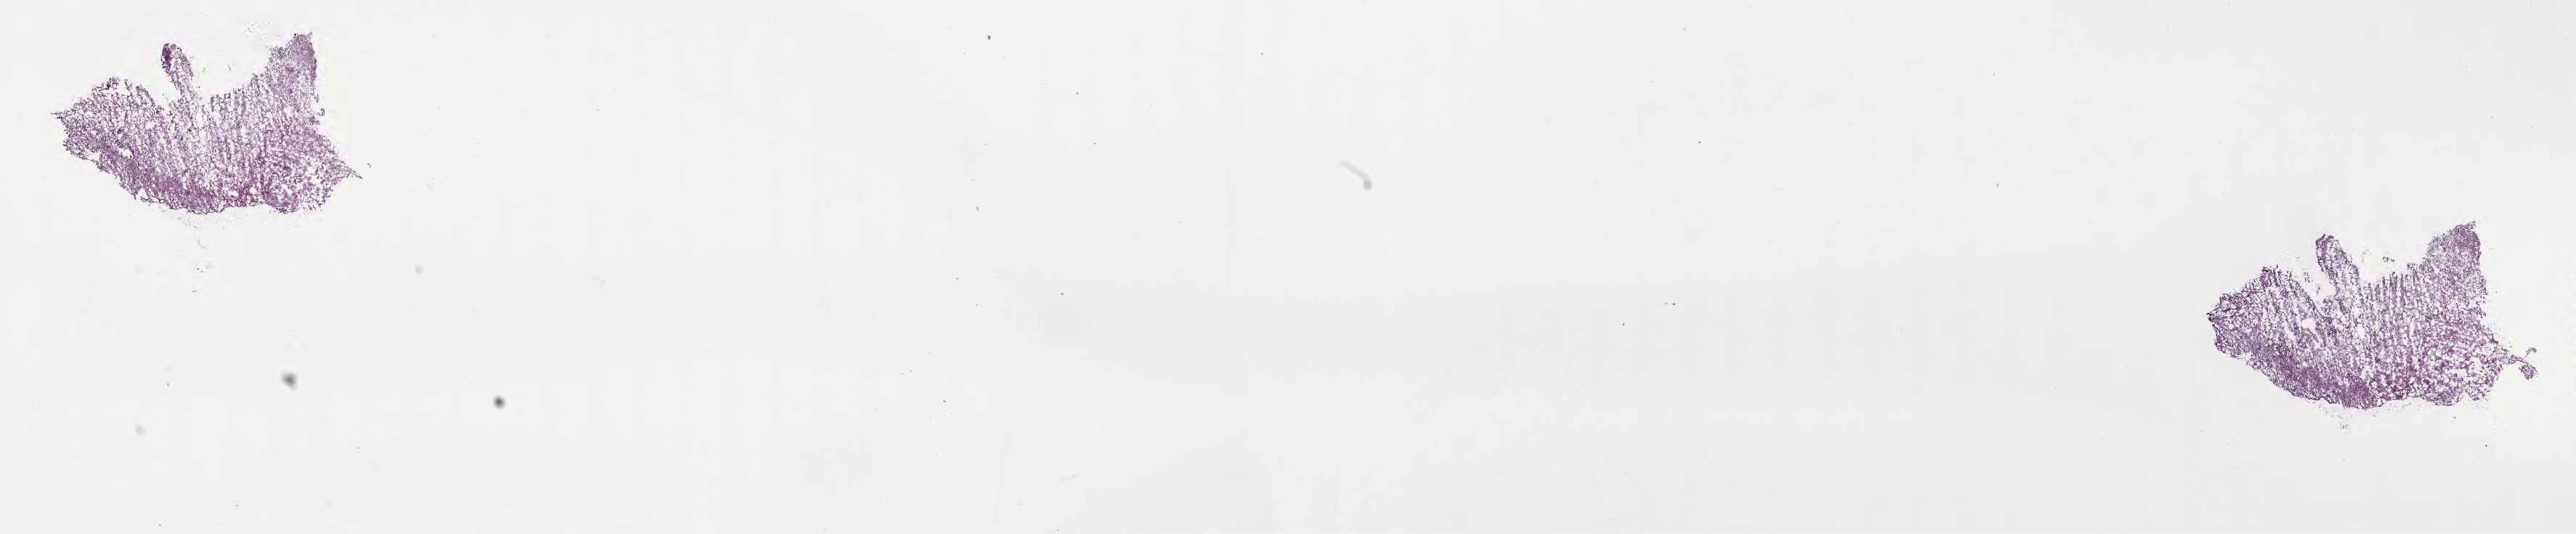
Whole-slide image, H&E stain of tumor tissue from the brain — a low-resolution overview of the entire scanned area, about 28.7 x 5.9 mm; frozen section. Patient male; age 45 months (3 years 9 months).
* diagnosis: Pilocytic astrocytoma